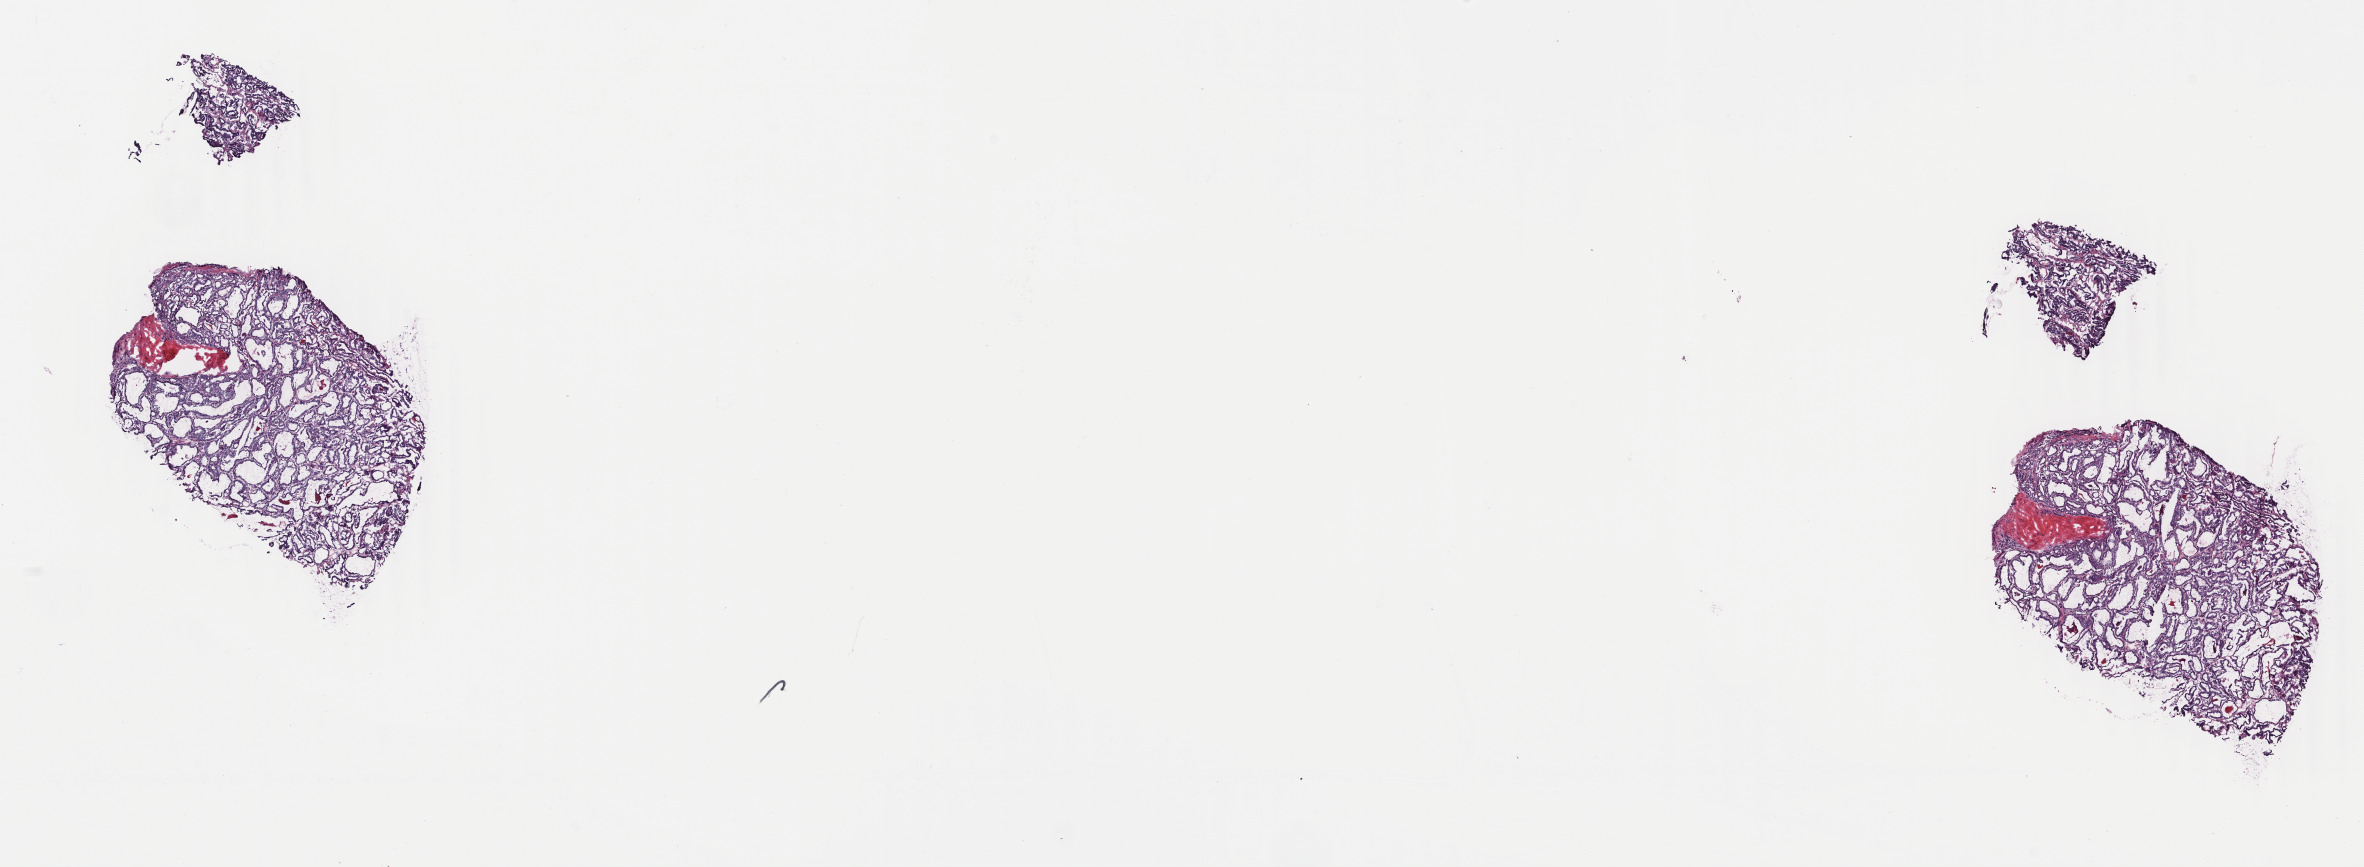
Hematoxylin and eosin (H&E) stained whole-slide image, shown as a low-resolution overview of the whole scanned area (about 18.8 x 6.9 mm, slide scanned at 40x). Frozen section from the top of the tissue portion. Thyroid, primary tumour sample. Female, age 64 years at initial diagnosis. Composition of this section per pathologist review: tumour cells 95%, tumour nuclei 80%.
Diagnosis: Papillary adenocarcinoma, NOS (thyroid gland).